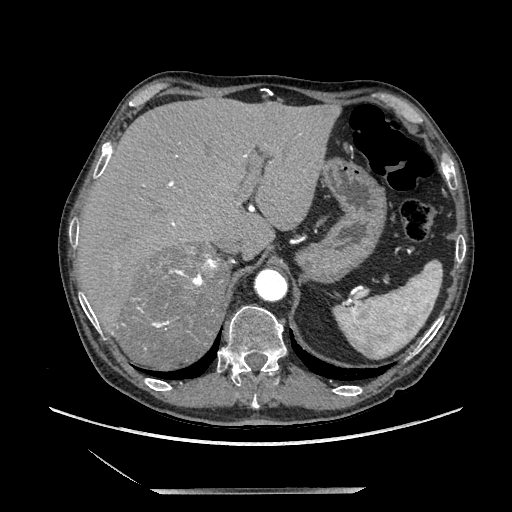
Contrast-enhanced abdominal CT, one axial slice; slice 160 of 243 in the series (ordered by position); soft-tissue window (W 400 / L 40 HU); 512 × 512 image matrix. Male patient. From the clinical record (not read from this slice): diagnosis: adrenocortical carcinoma; tumour side: right adrenal; tumour size at pathology: 16 cm; Ki-67 index: 17 %; stage (as recorded): 3.
Outlined on this slice (semi-automatically segmented with operator editing):
- mass: box from (x=121, y=246) to (x=228, y=368) px